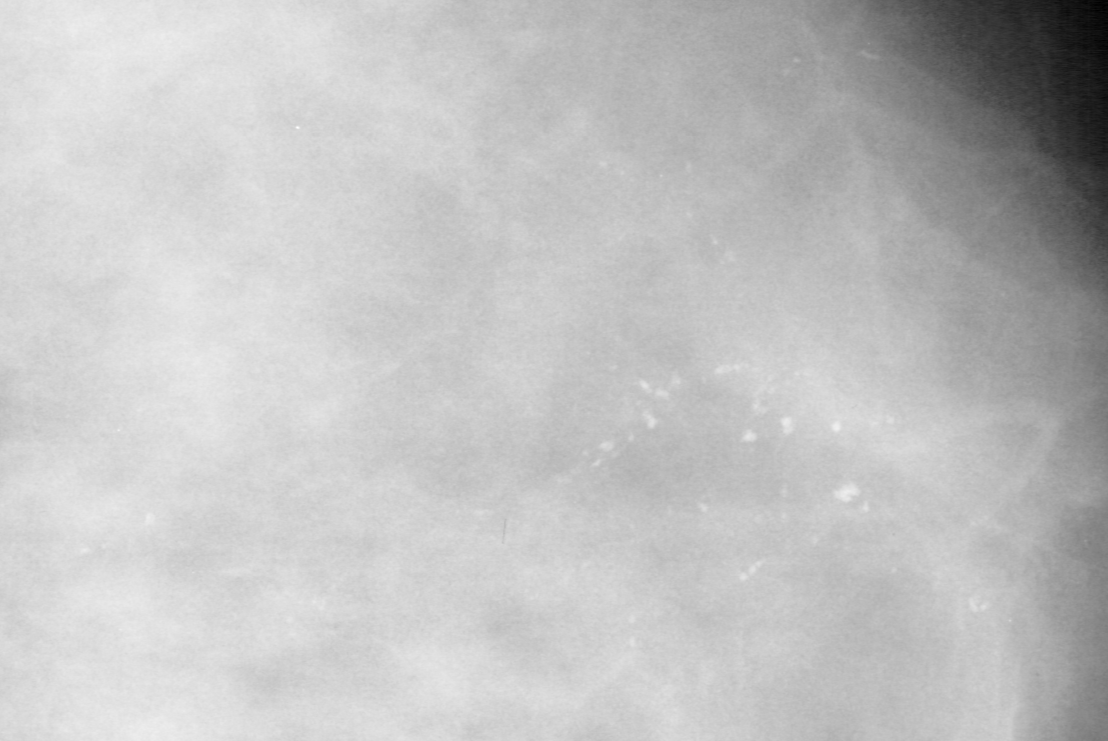
Crop from a digitized film mammogram around one marked abnormality, right breast, CC view, BI-RADS breast density category 4 (scale 1–4).
- Finding: calcifications, morphology pleomorphic, distribution segmental; BI-RADS assessment category 5; pathology (as recorded): malignant.